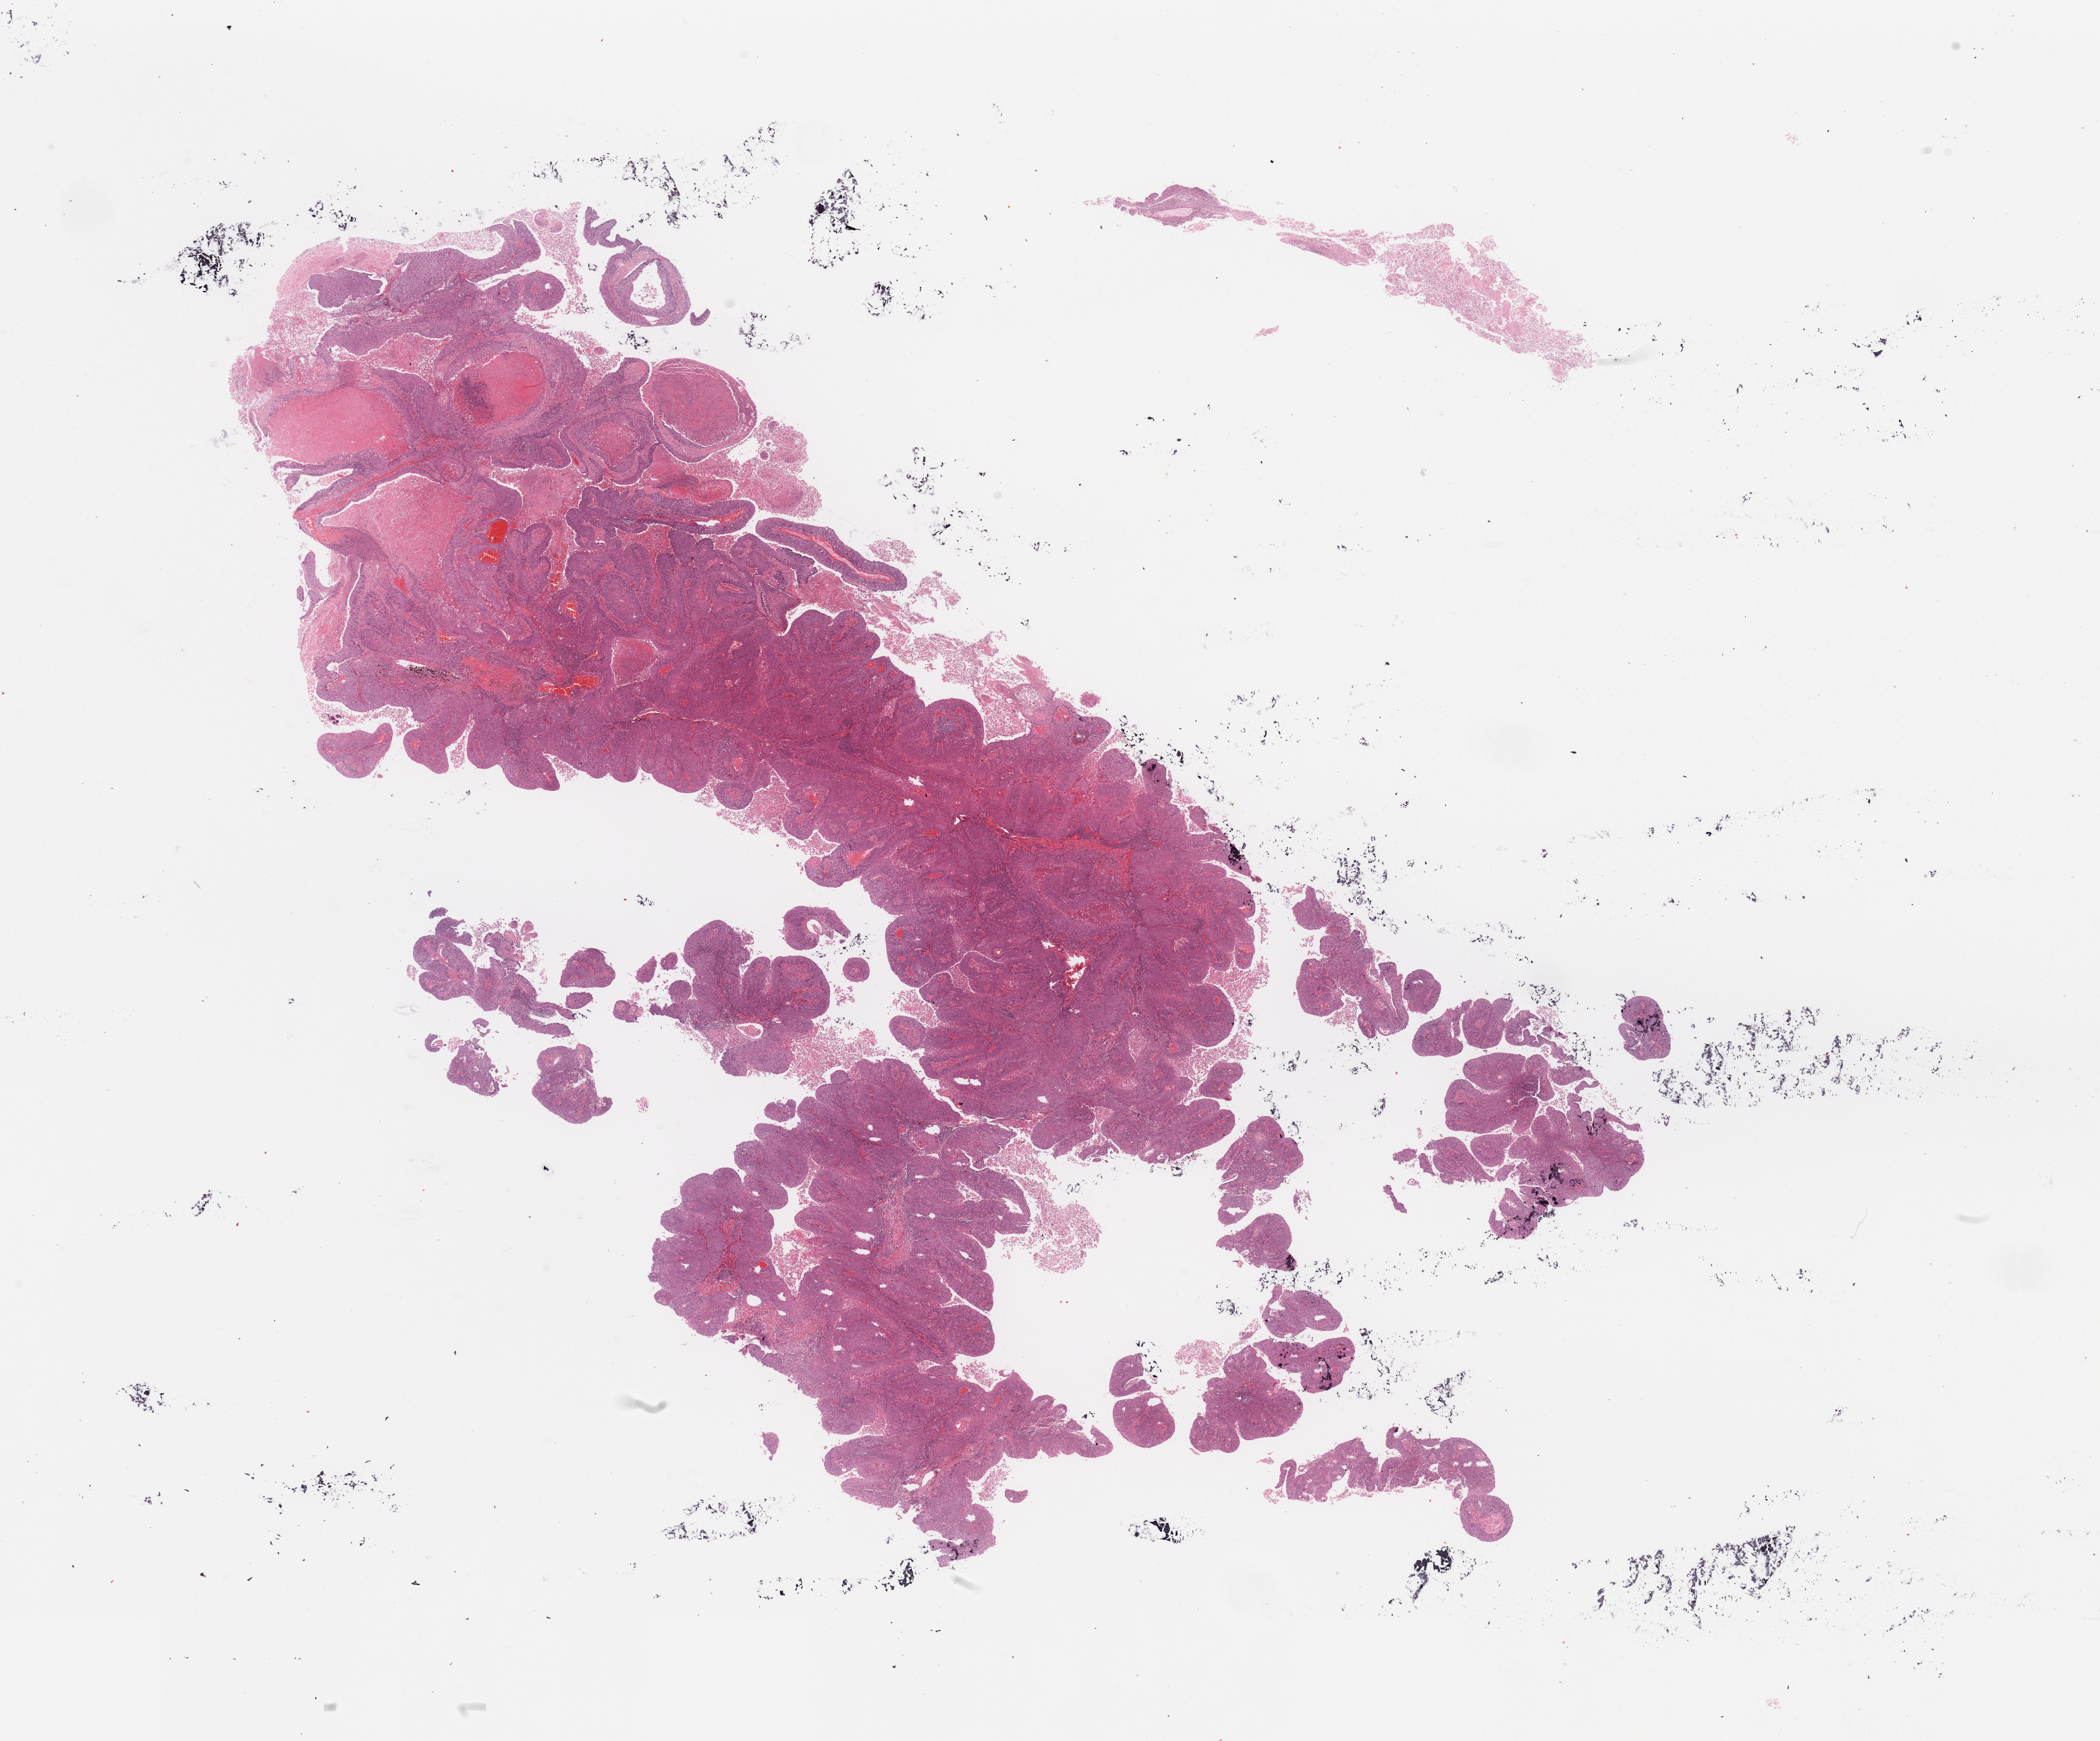
Digitized H&E tissue section (whole slide), whole scanned area (about 24.6 x 20.4 mm, slide scanned at 20x) shown as a low-resolution overview. Tumour tissue sample, sampled site: lung. 61-year-old male patient. Histologic grade: G3 (poorly differentiated). Slide review estimates, as recorded: tumour nuclei 70%, necrosis 20%.
Diagnosis: Squamous cell carcinoma, NOS. AJCC pathologic stage: IIA. Primary tumour site (as recorded): left upper lobe.